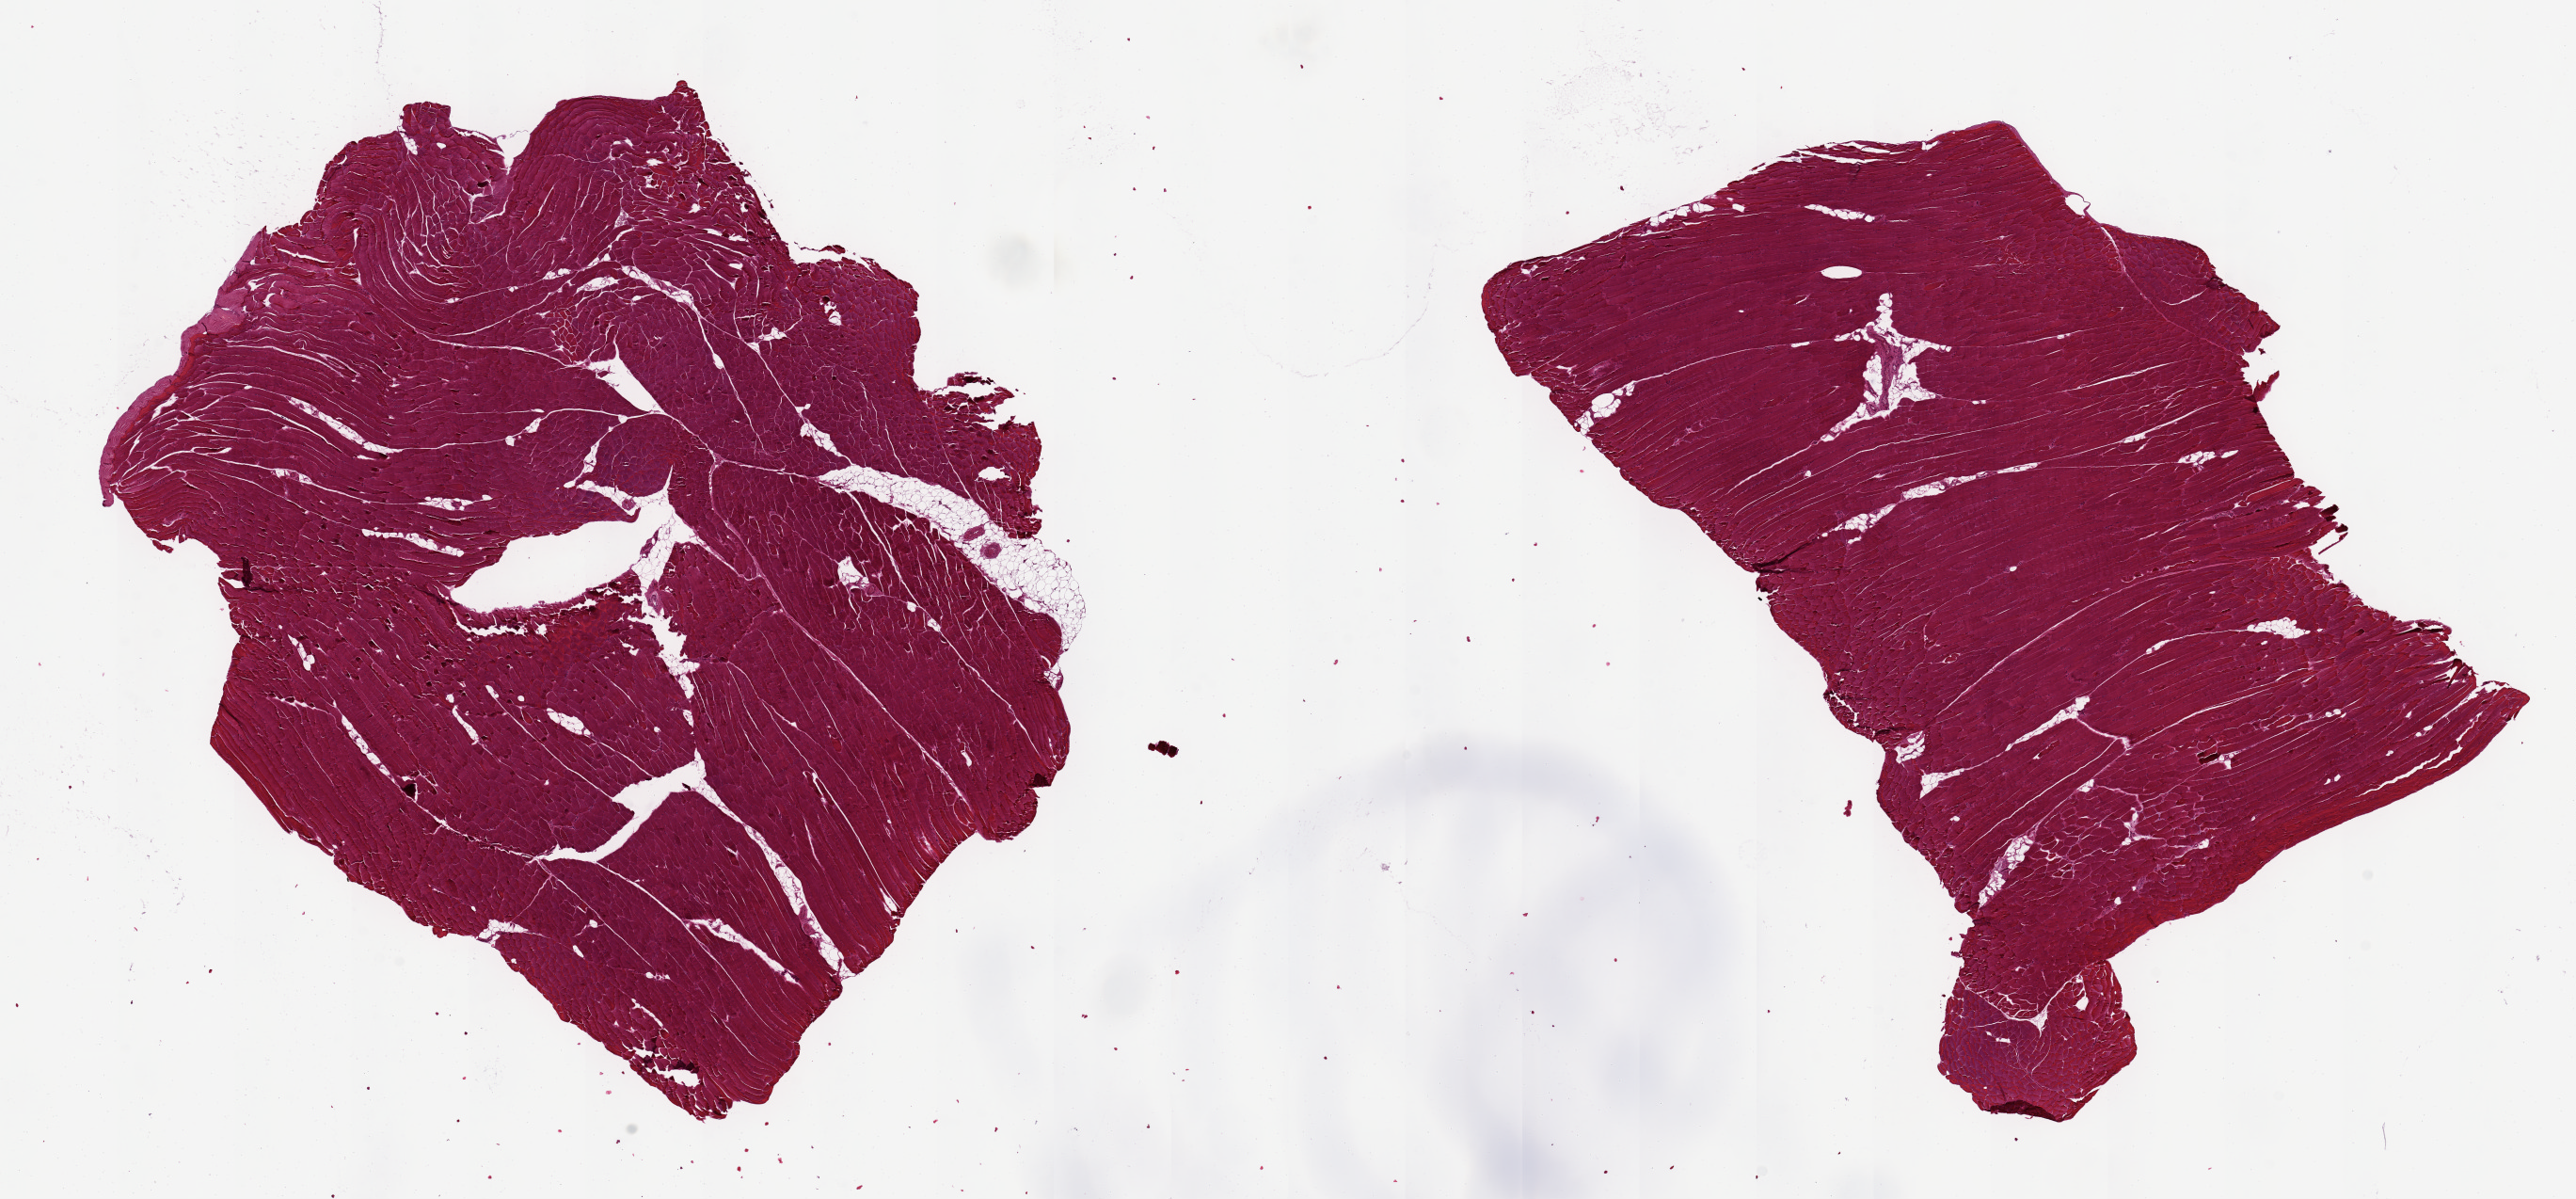
Digitized haematoxylin and eosin-stained section, a low-resolution overview of the entire scanned area, about 21.7 x 10.1 mm, PAXgene-fixed, paraffin-embedded tissue, target tissue: skeletal muscle, donor tissue sample. Donor sex: male.
Pathologist's review note for this sample: 2 pieces 6x6 & 7x7 mm;<5% internal adipose.